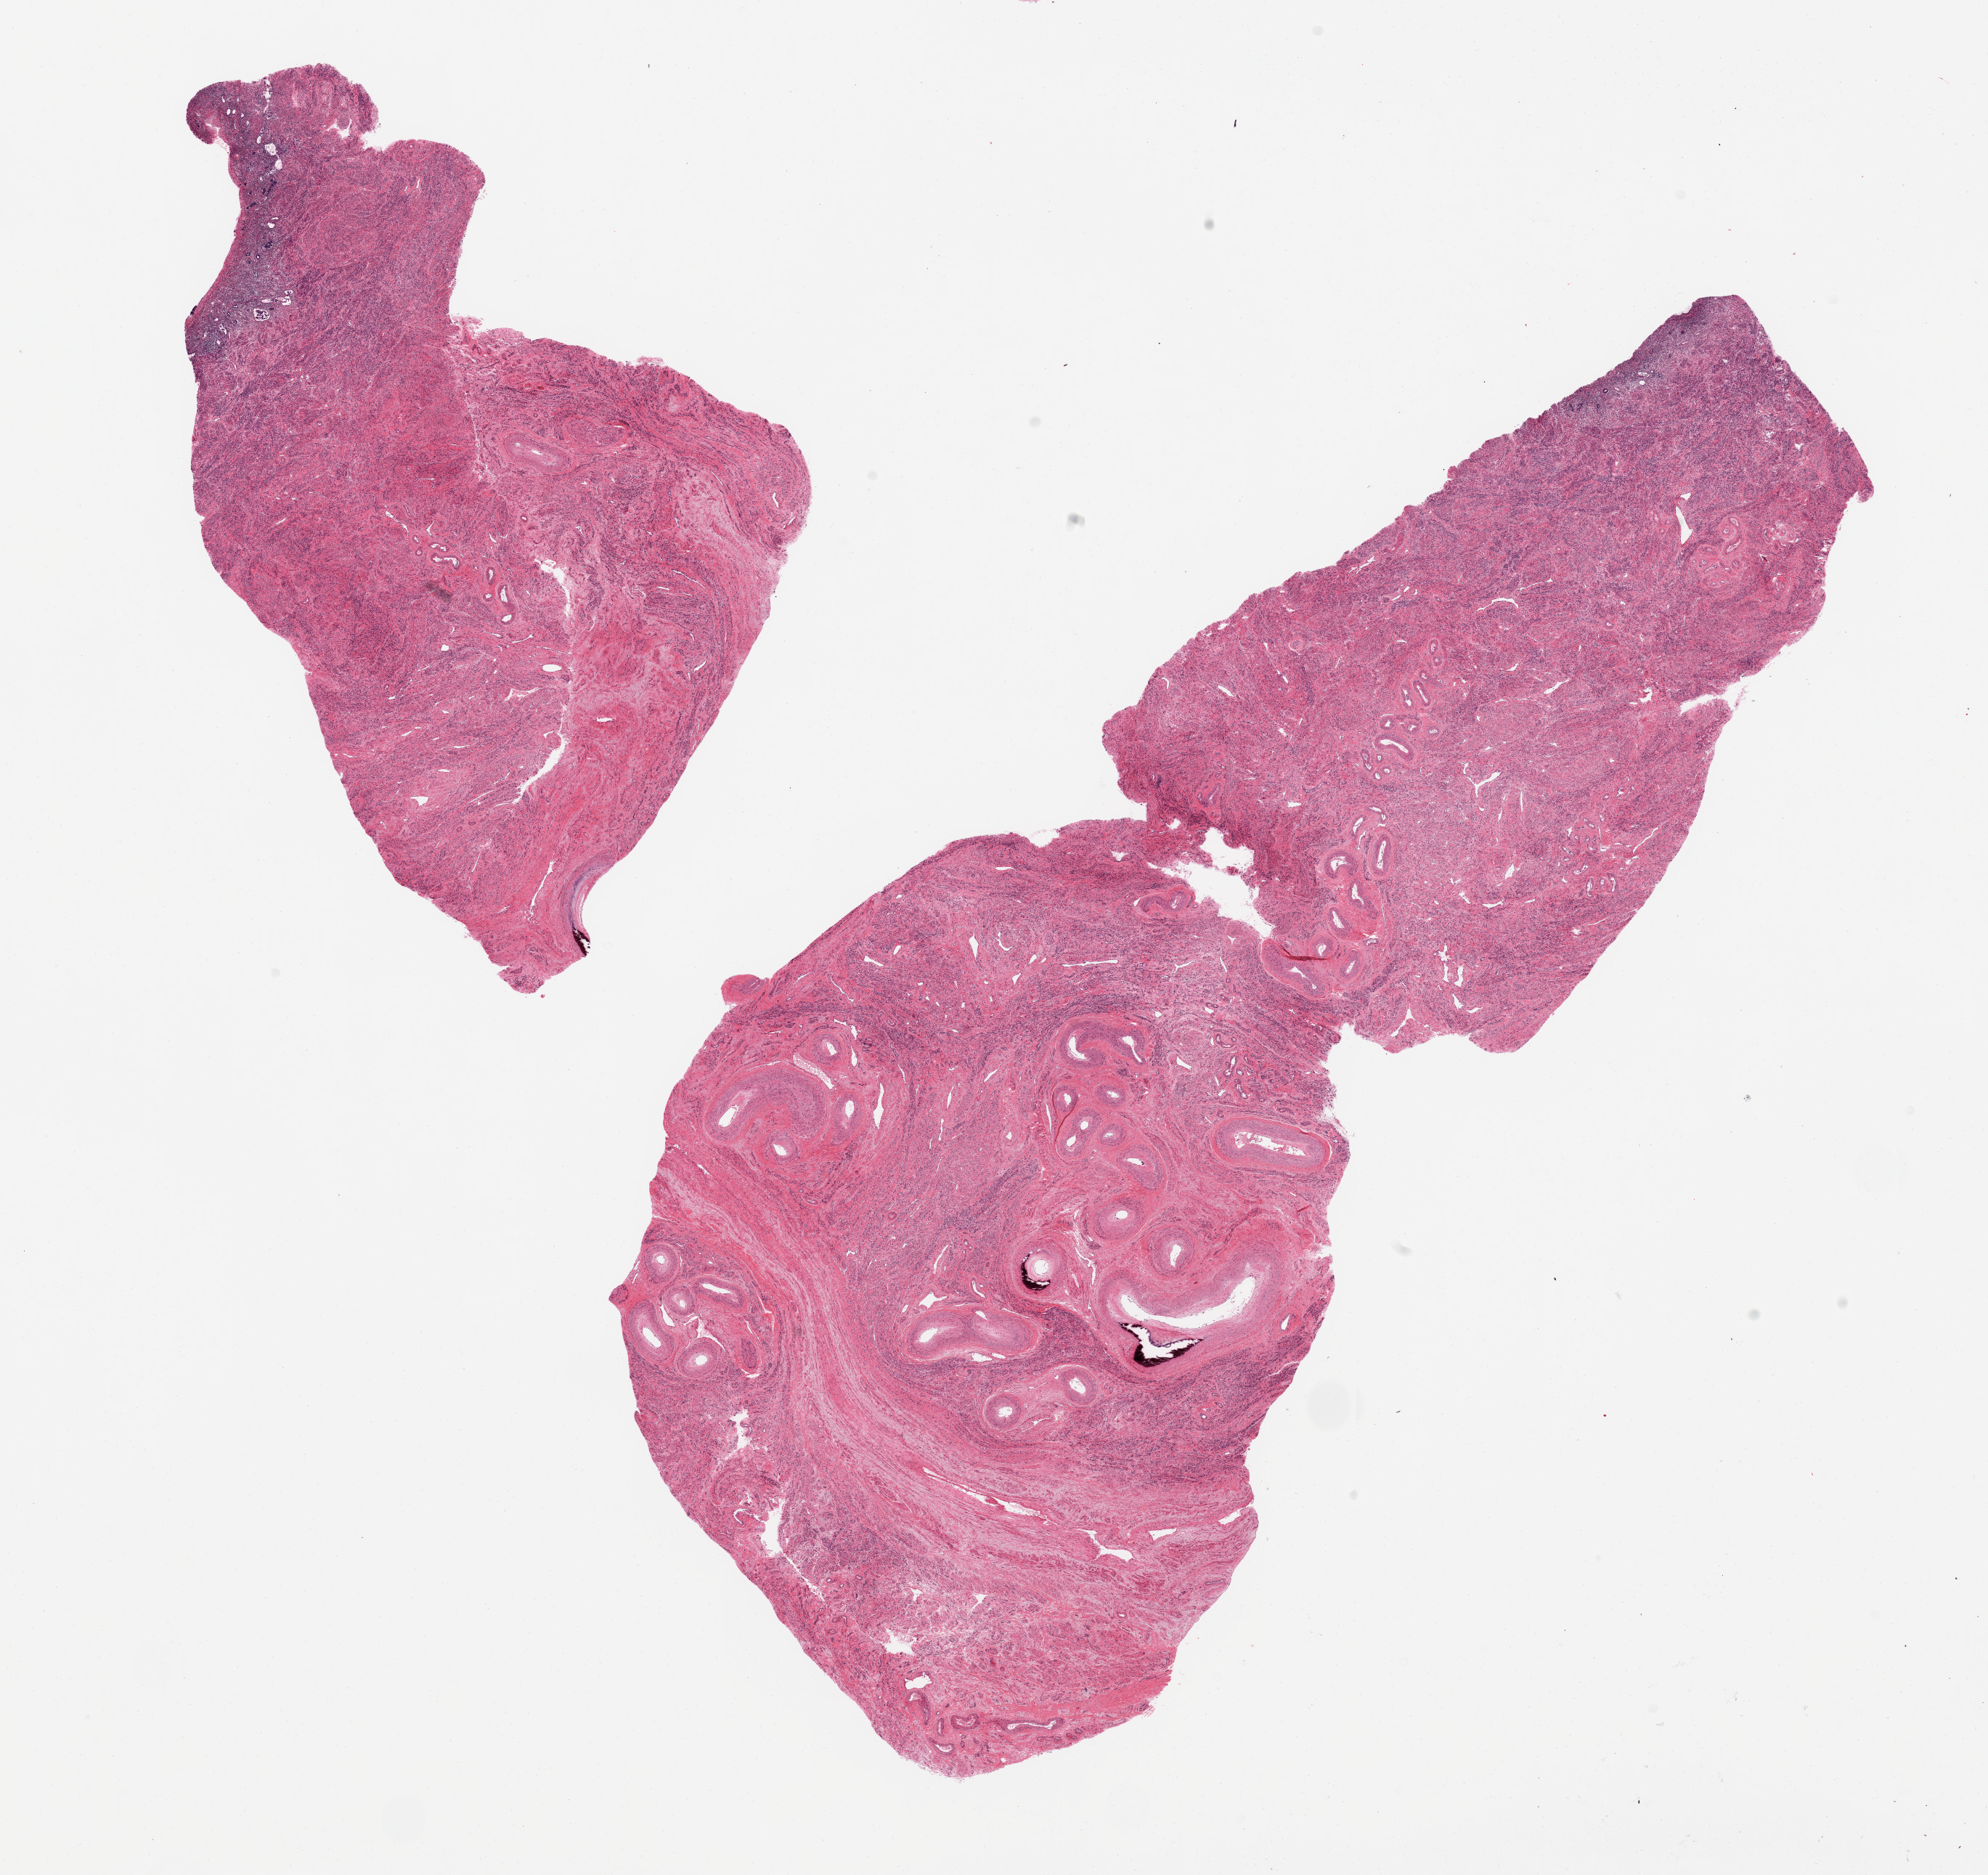
Digitized H&E-stained section, shown as a low-resolution overview of the whole scanned area (about 21.7 x 20.4 mm), PAXgene-fixed paraffin-embedded (PFPE) section, sampled site (target tissue): uterus, donor tissue sample. Female donor.
• pathologist's review note for this sample: 2 pieces